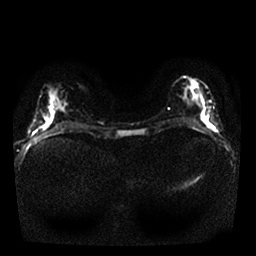
Breast MRI, one axial slice; position 12 of 25 along the scan axis; diffusion-weighted series; image 2 of 4 stored at this slice position (different b-values; order by instance number); 1.5 T; 256 × 256 image matrix, field of view 320 × 320 mm. Female patient.
Outlined on this slice (outlined manually by an expert reader):
- tumour on diffusion-weighted imaging: box from (x=204, y=119) to (x=210, y=126) px